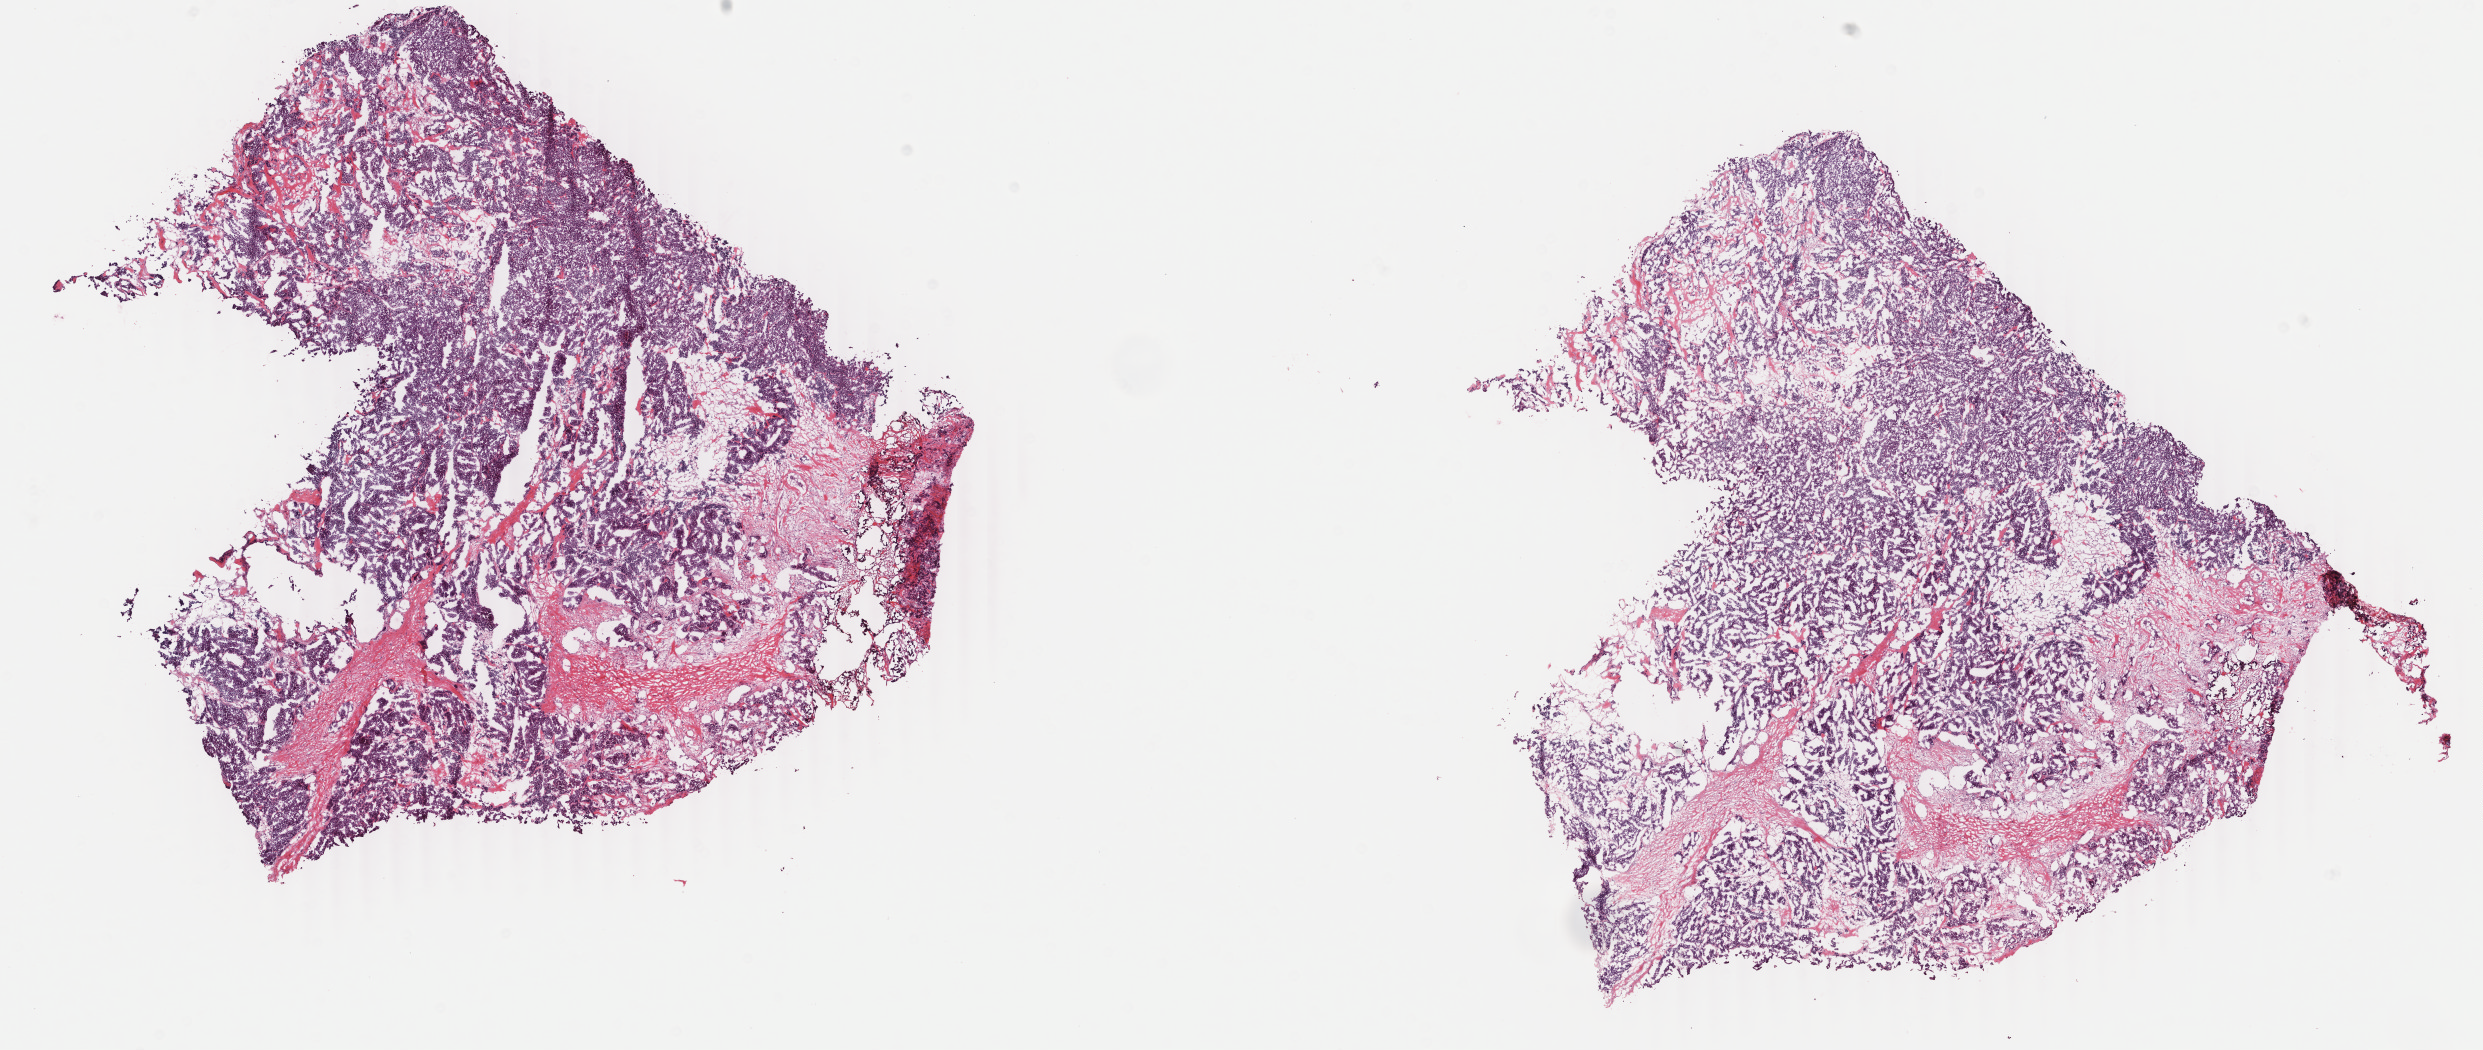
H&E-stained whole-slide image — low-resolution overview of the scanned area, about 19.8 x 8.4 mm; frozen section from the top of the tissue portion; breast, primary tumour sample. Female, age 62 years at initial diagnosis. Composition of this section per pathologist review: tumour cells 80%, tumour nuclei 80%.
Diagnosis: Infiltrating duct carcinoma, NOS.